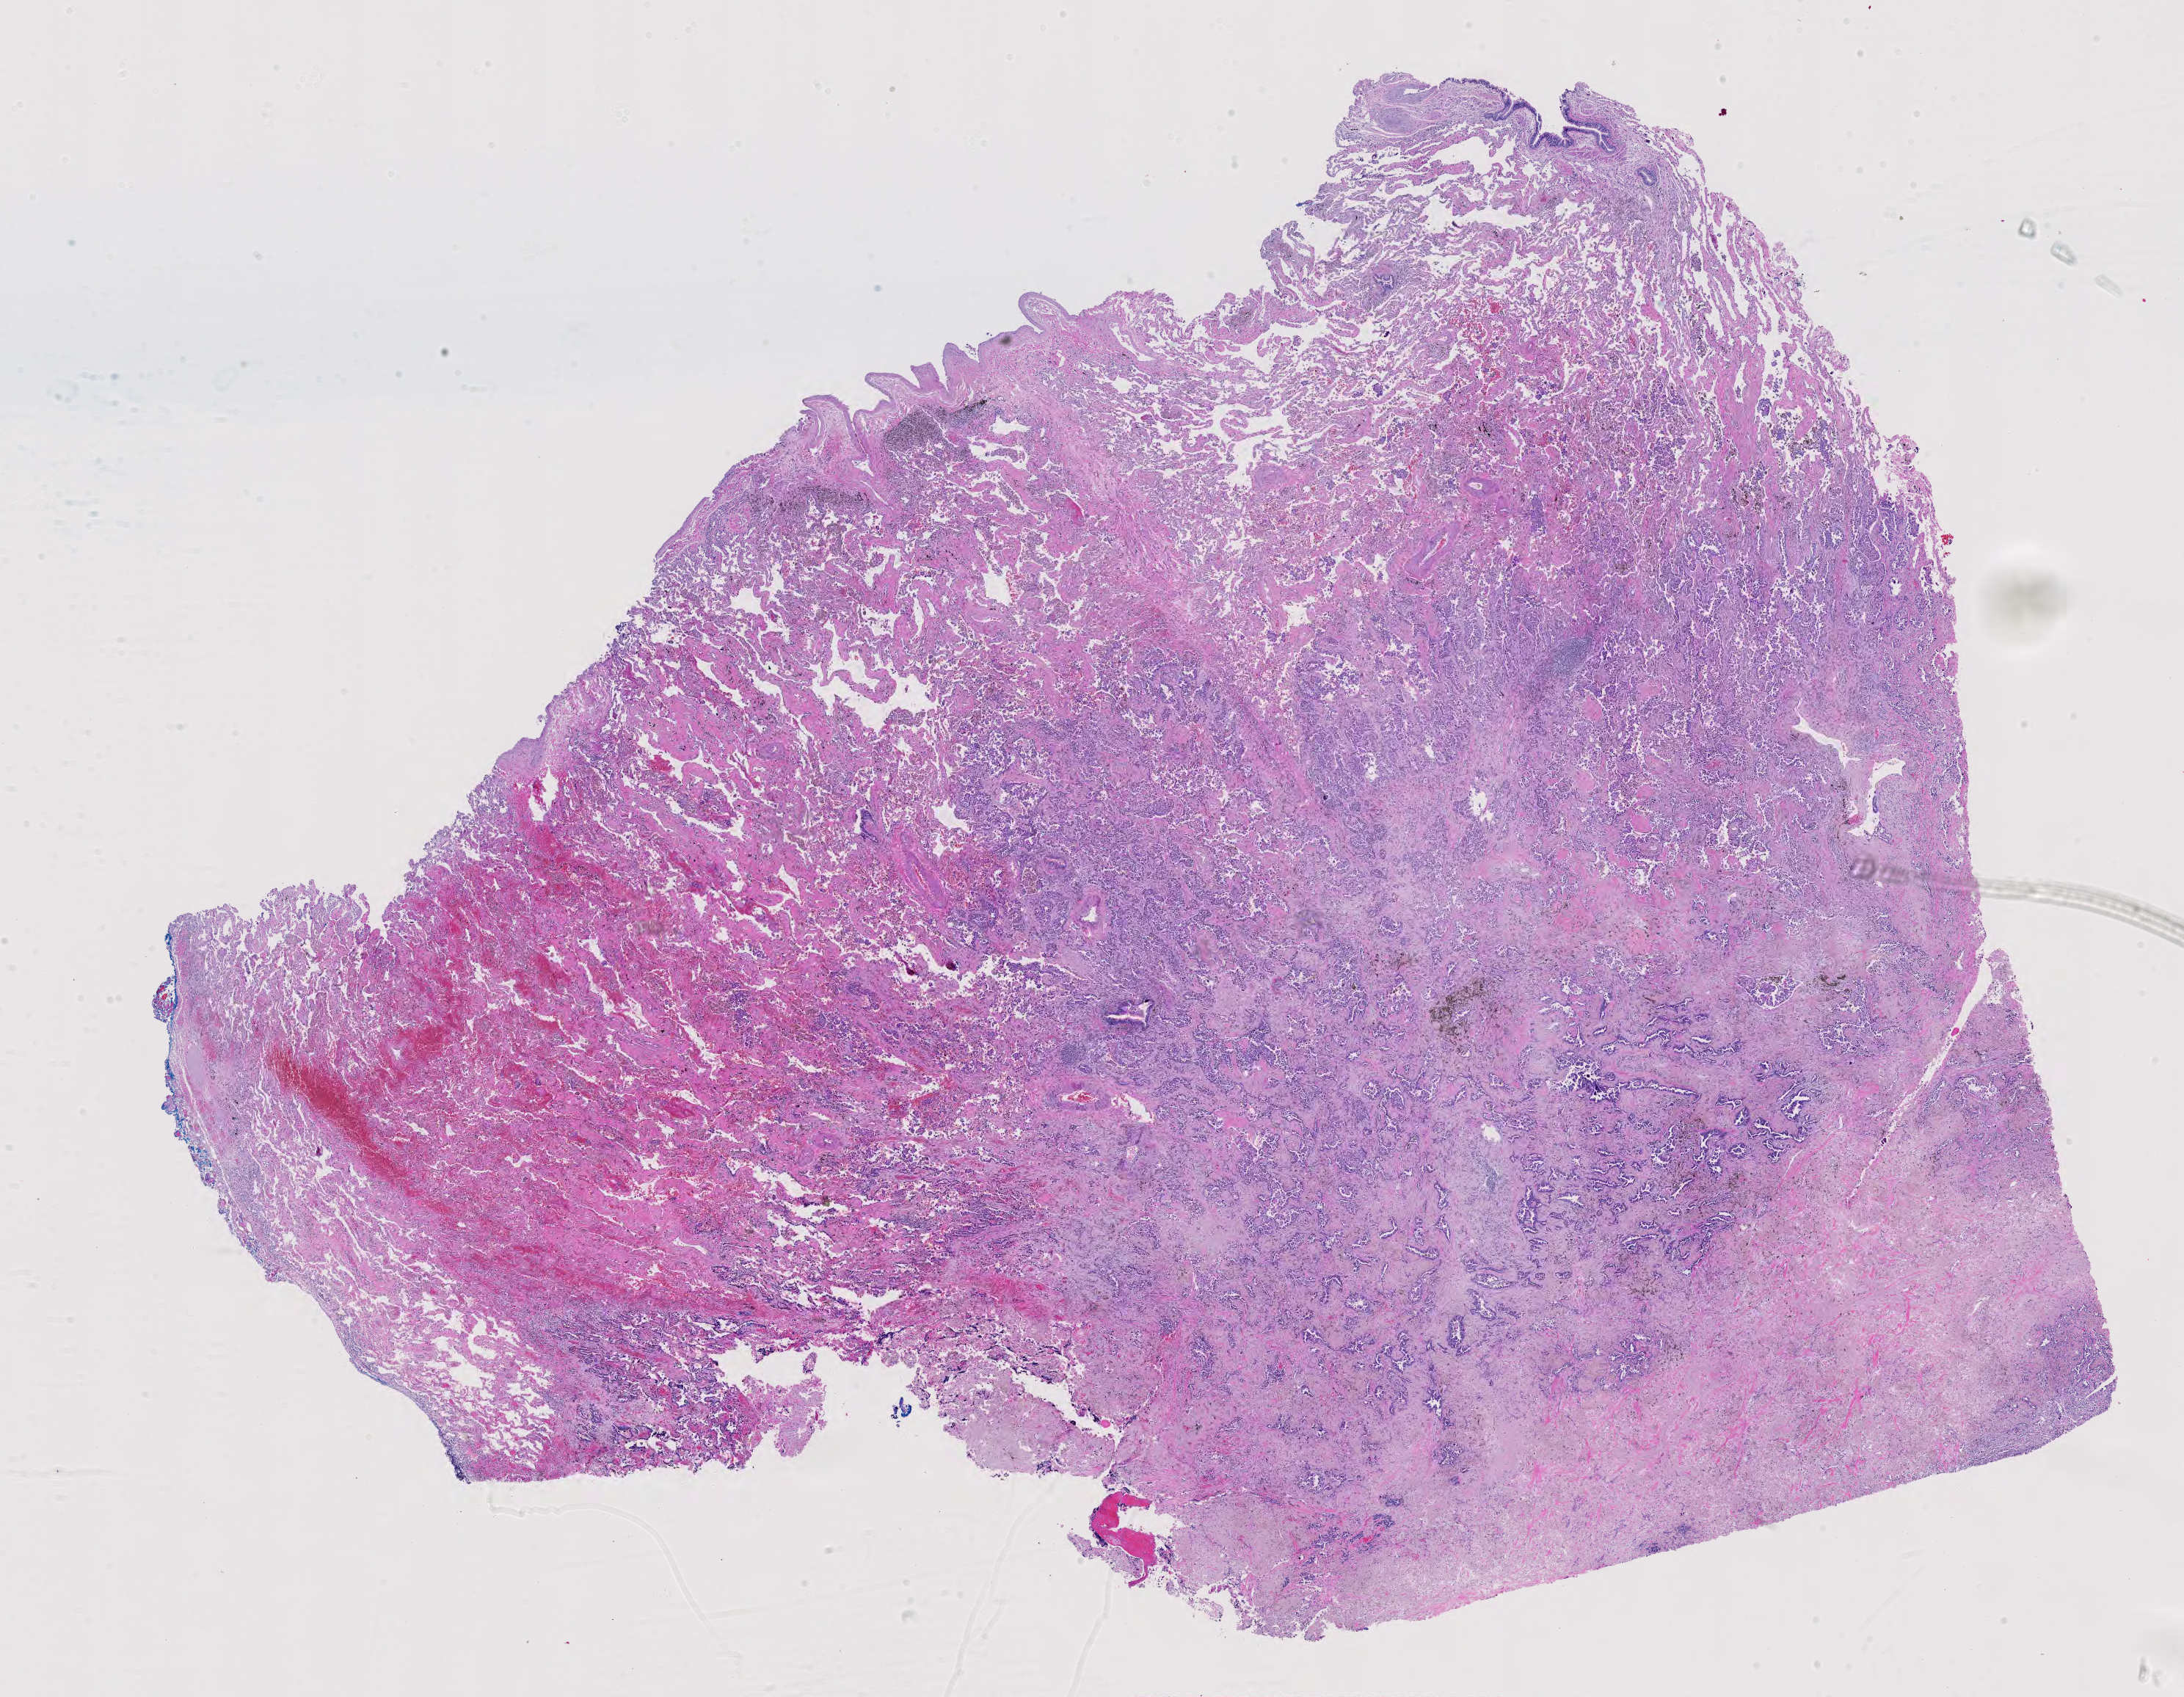
H&E-stained whole-slide image — a low-resolution overview of the entire scanned area, about 21.6 x 16.8 mm (slide scanned at 40x), FFPE section, primary tumour sample from the lung. Female patient; age at initial diagnosis 54 years.
Pathologic diagnosis: Adenocarcinoma, NOS.